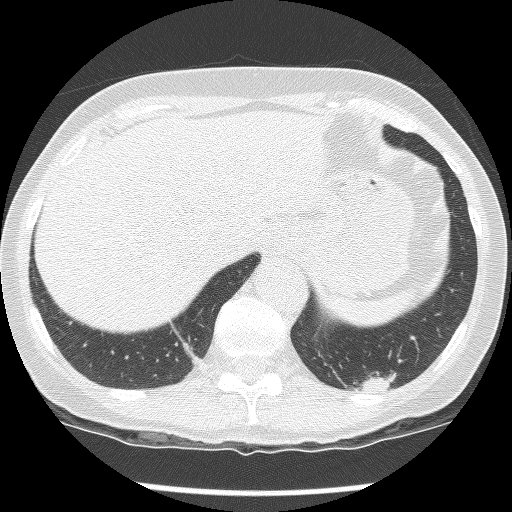
Axial slice from a low-dose chest CT screening exam; second screening round (one year after baseline); lung window (W 1500 / L -600 HU); slice 108 of 136 in the series; 512 × 512 image matrix. Female participant, aged 61 years at enrolment. Current smoker at enrolment.
Expert reader's lesion annotation, bounding box (x1, y1, x2, y2) in pixels: (326, 306, 441, 411). The screening reader recorded 2 non-calcified nodules or masses ≥4 mm on this exam (left lower lobe, left lower lobe); which of them this box marks is not recorded. Official screen result: positive, no significant change: stable abnormalities potentially related to lung cancer, unchanged since the prior screening exam. Later outcome: lung cancer diagnosed 585 days after this screen (after the third annual screen) — non-small cell carcinoma, left lower lobe, poorly differentiated (G3), stage IB (AJCC 6th edition), 100 mm at pathology.